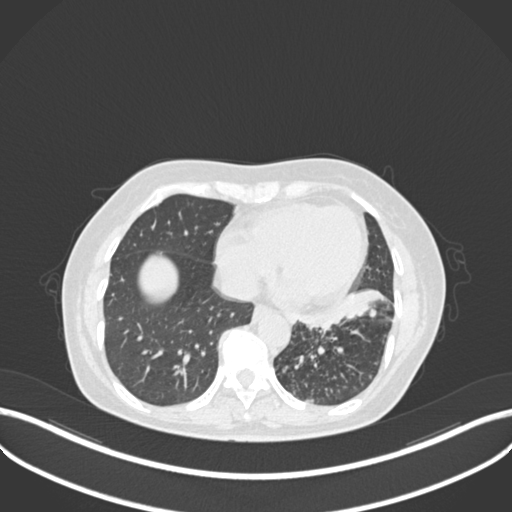
Chest CT, one axial slice. Reconstruction kernel B30f. Lung window (W 1500 / L -600 HU). 1 mm slice thickness. 512 × 512 image matrix, field of view 400 × 400 mm. Female patient, age 63 years. Case-level facts recorded for this patient, not image findings: clinical TNM (as recorded): T1b N0 M0; histopathological grade: G2-3.
Outlined on this slice (rectangle marked by the reading radiologist):
- lung tumour (recorded histology: adenocarcinoma): bounding box (x1, y1, x2, y2) in pixels: (294, 284, 392, 329)